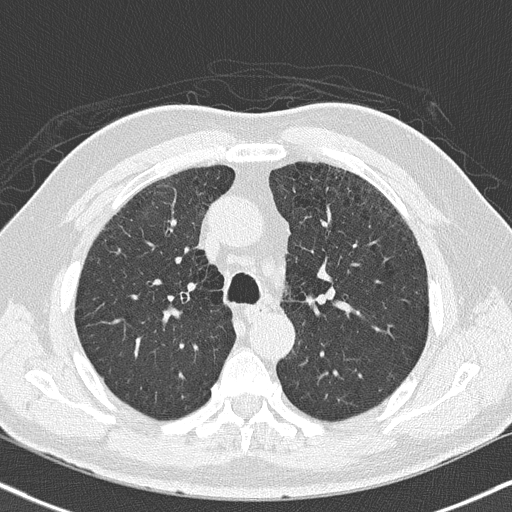
Axial slice from a low-dose chest CT screening exam. Second screening round (one year after baseline). Lung window (W 1500 / L -600 HU). 2 mm slice thickness. 120 kVp. Male, age 64 years at enrolment. Current smoker at enrolment.
Lesion marked by an expert reader, box from (x=311, y=285) to (x=344, y=312) px. No non-calcified nodule or mass ≥4 mm was recorded by the screening reader at this exam. Official screen result: positive, other. Participant outcome: lung cancer diagnosed 72 days after this screen — squamous cell carcinoma, keratinizing, NOS, left upper lobe, moderately differentiated (G2), stage IA (AJCC 6th edition), 4 mm at pathology.